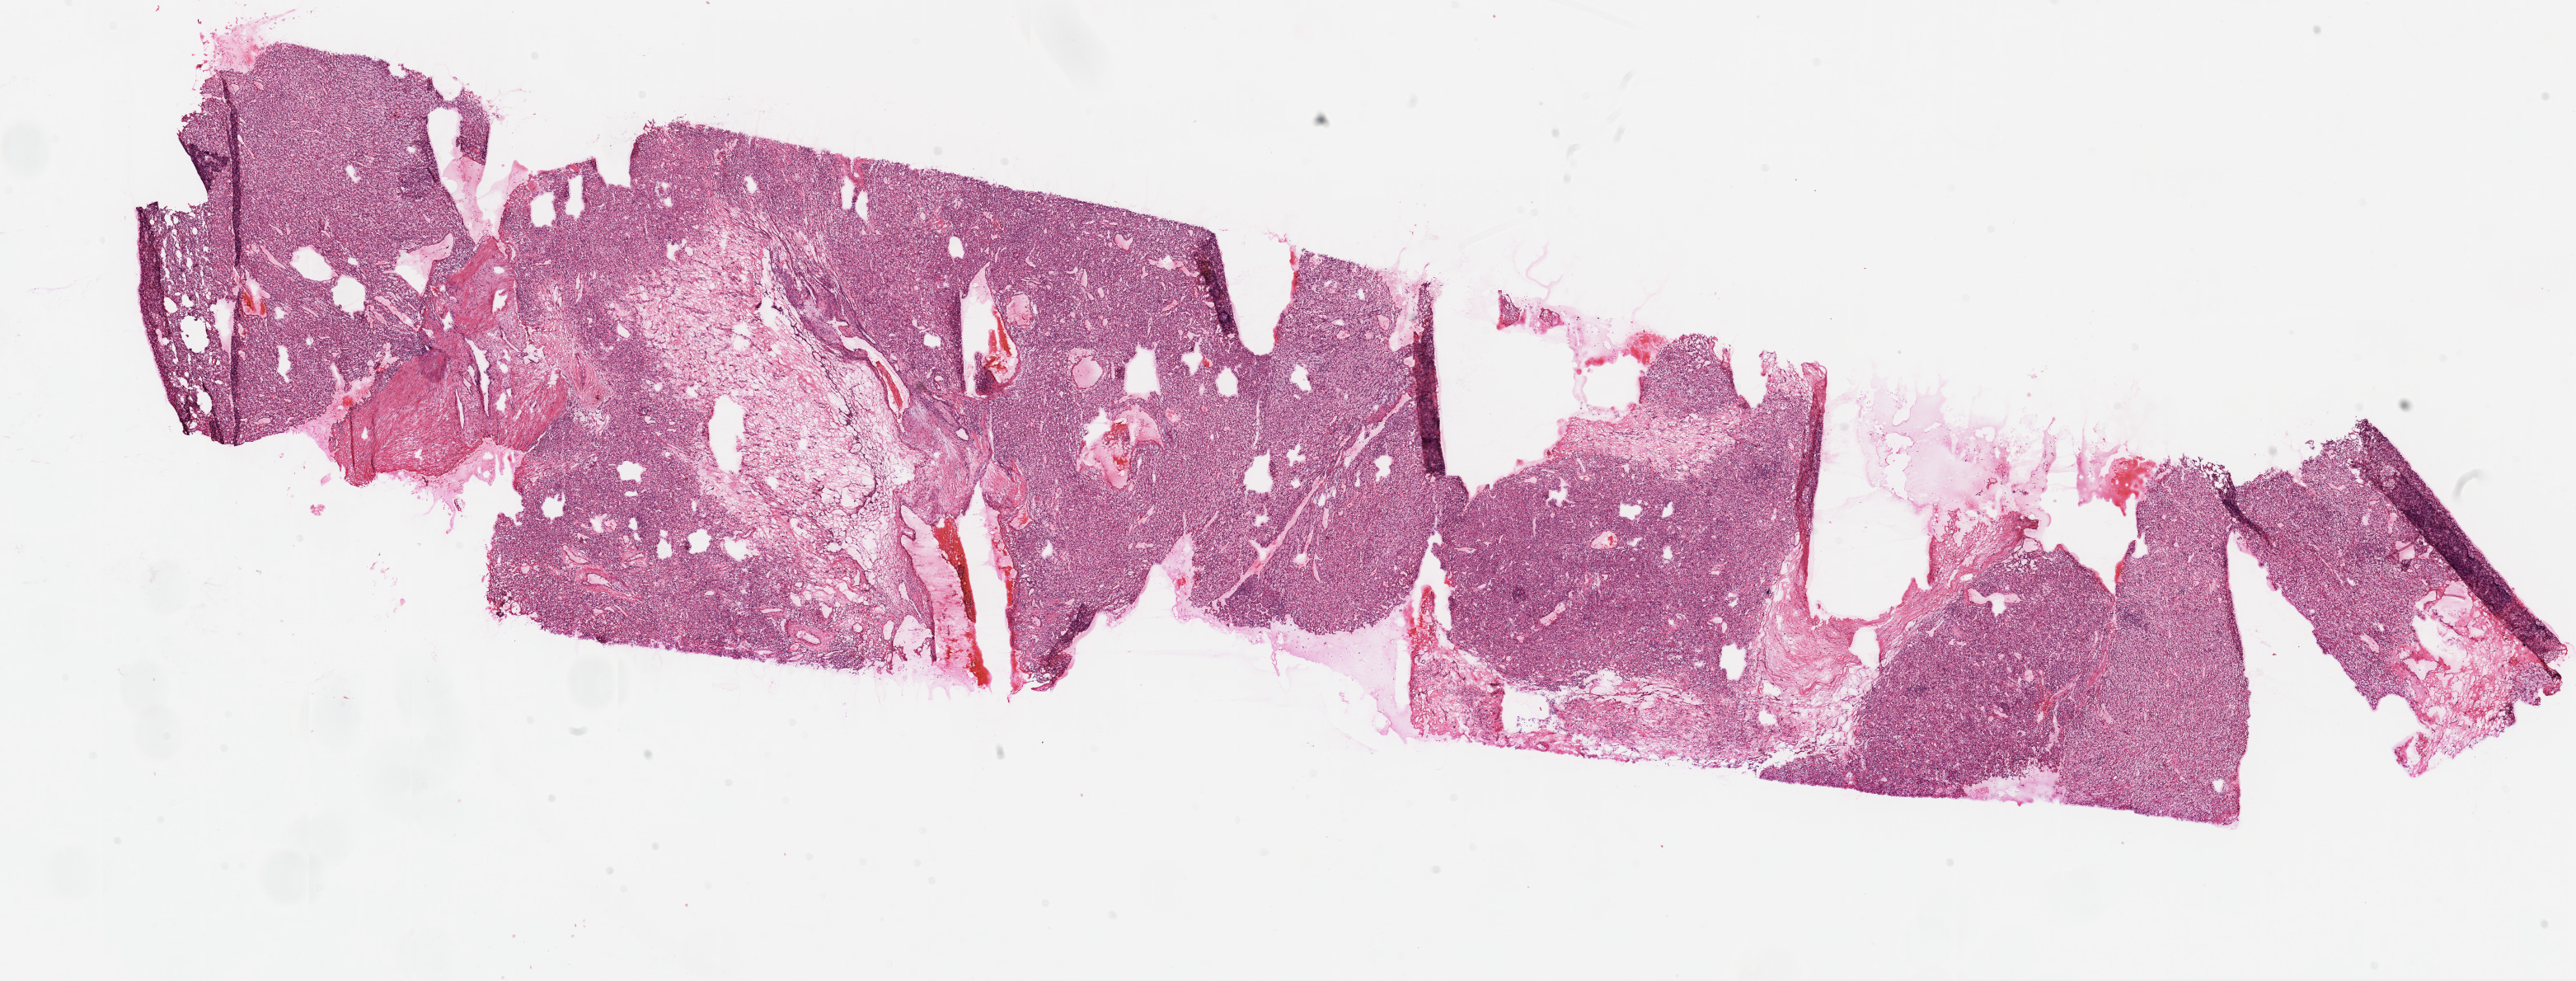
Whole-slide histology image, H&E-stained — shown as a low-resolution overview of the whole scanned area (about 25.1 x 9.5 mm). Frozen section from the top of the tissue portion. Primary tumour sample from the kidney. Female, age 67 years at initial diagnosis. Histologic grade: G3 (poorly differentiated). Slide review estimates, as recorded: tumour cells 95%, tumour nuclei 85%, normal cells 0%, stromal cells 5%, necrosis 0%.
AJCC pathologic stage: II. Histologic diagnosis: Clear cell adenocarcinoma, NOS.